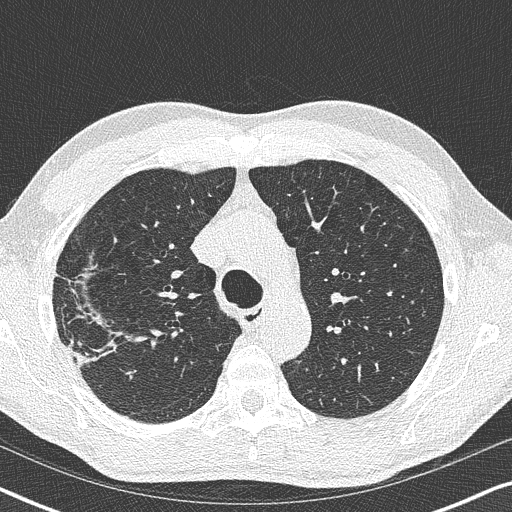
Low-dose screening chest CT, one axial slice; slice 266 of 356 in the series (ordered by position); reconstruction kernel B50f; 120 kVp; lung window (W 1500 / L -600 HU); 1 mm slice thickness; 512 × 512 image matrix, field of view 330 × 330 mm.
Outlined on this slice (manually delineated by an expert):
- lesion 1 (tumor, upper lobe of right lung): bounding box <68,341,92,366> (left, top, right, bottom; pixels)